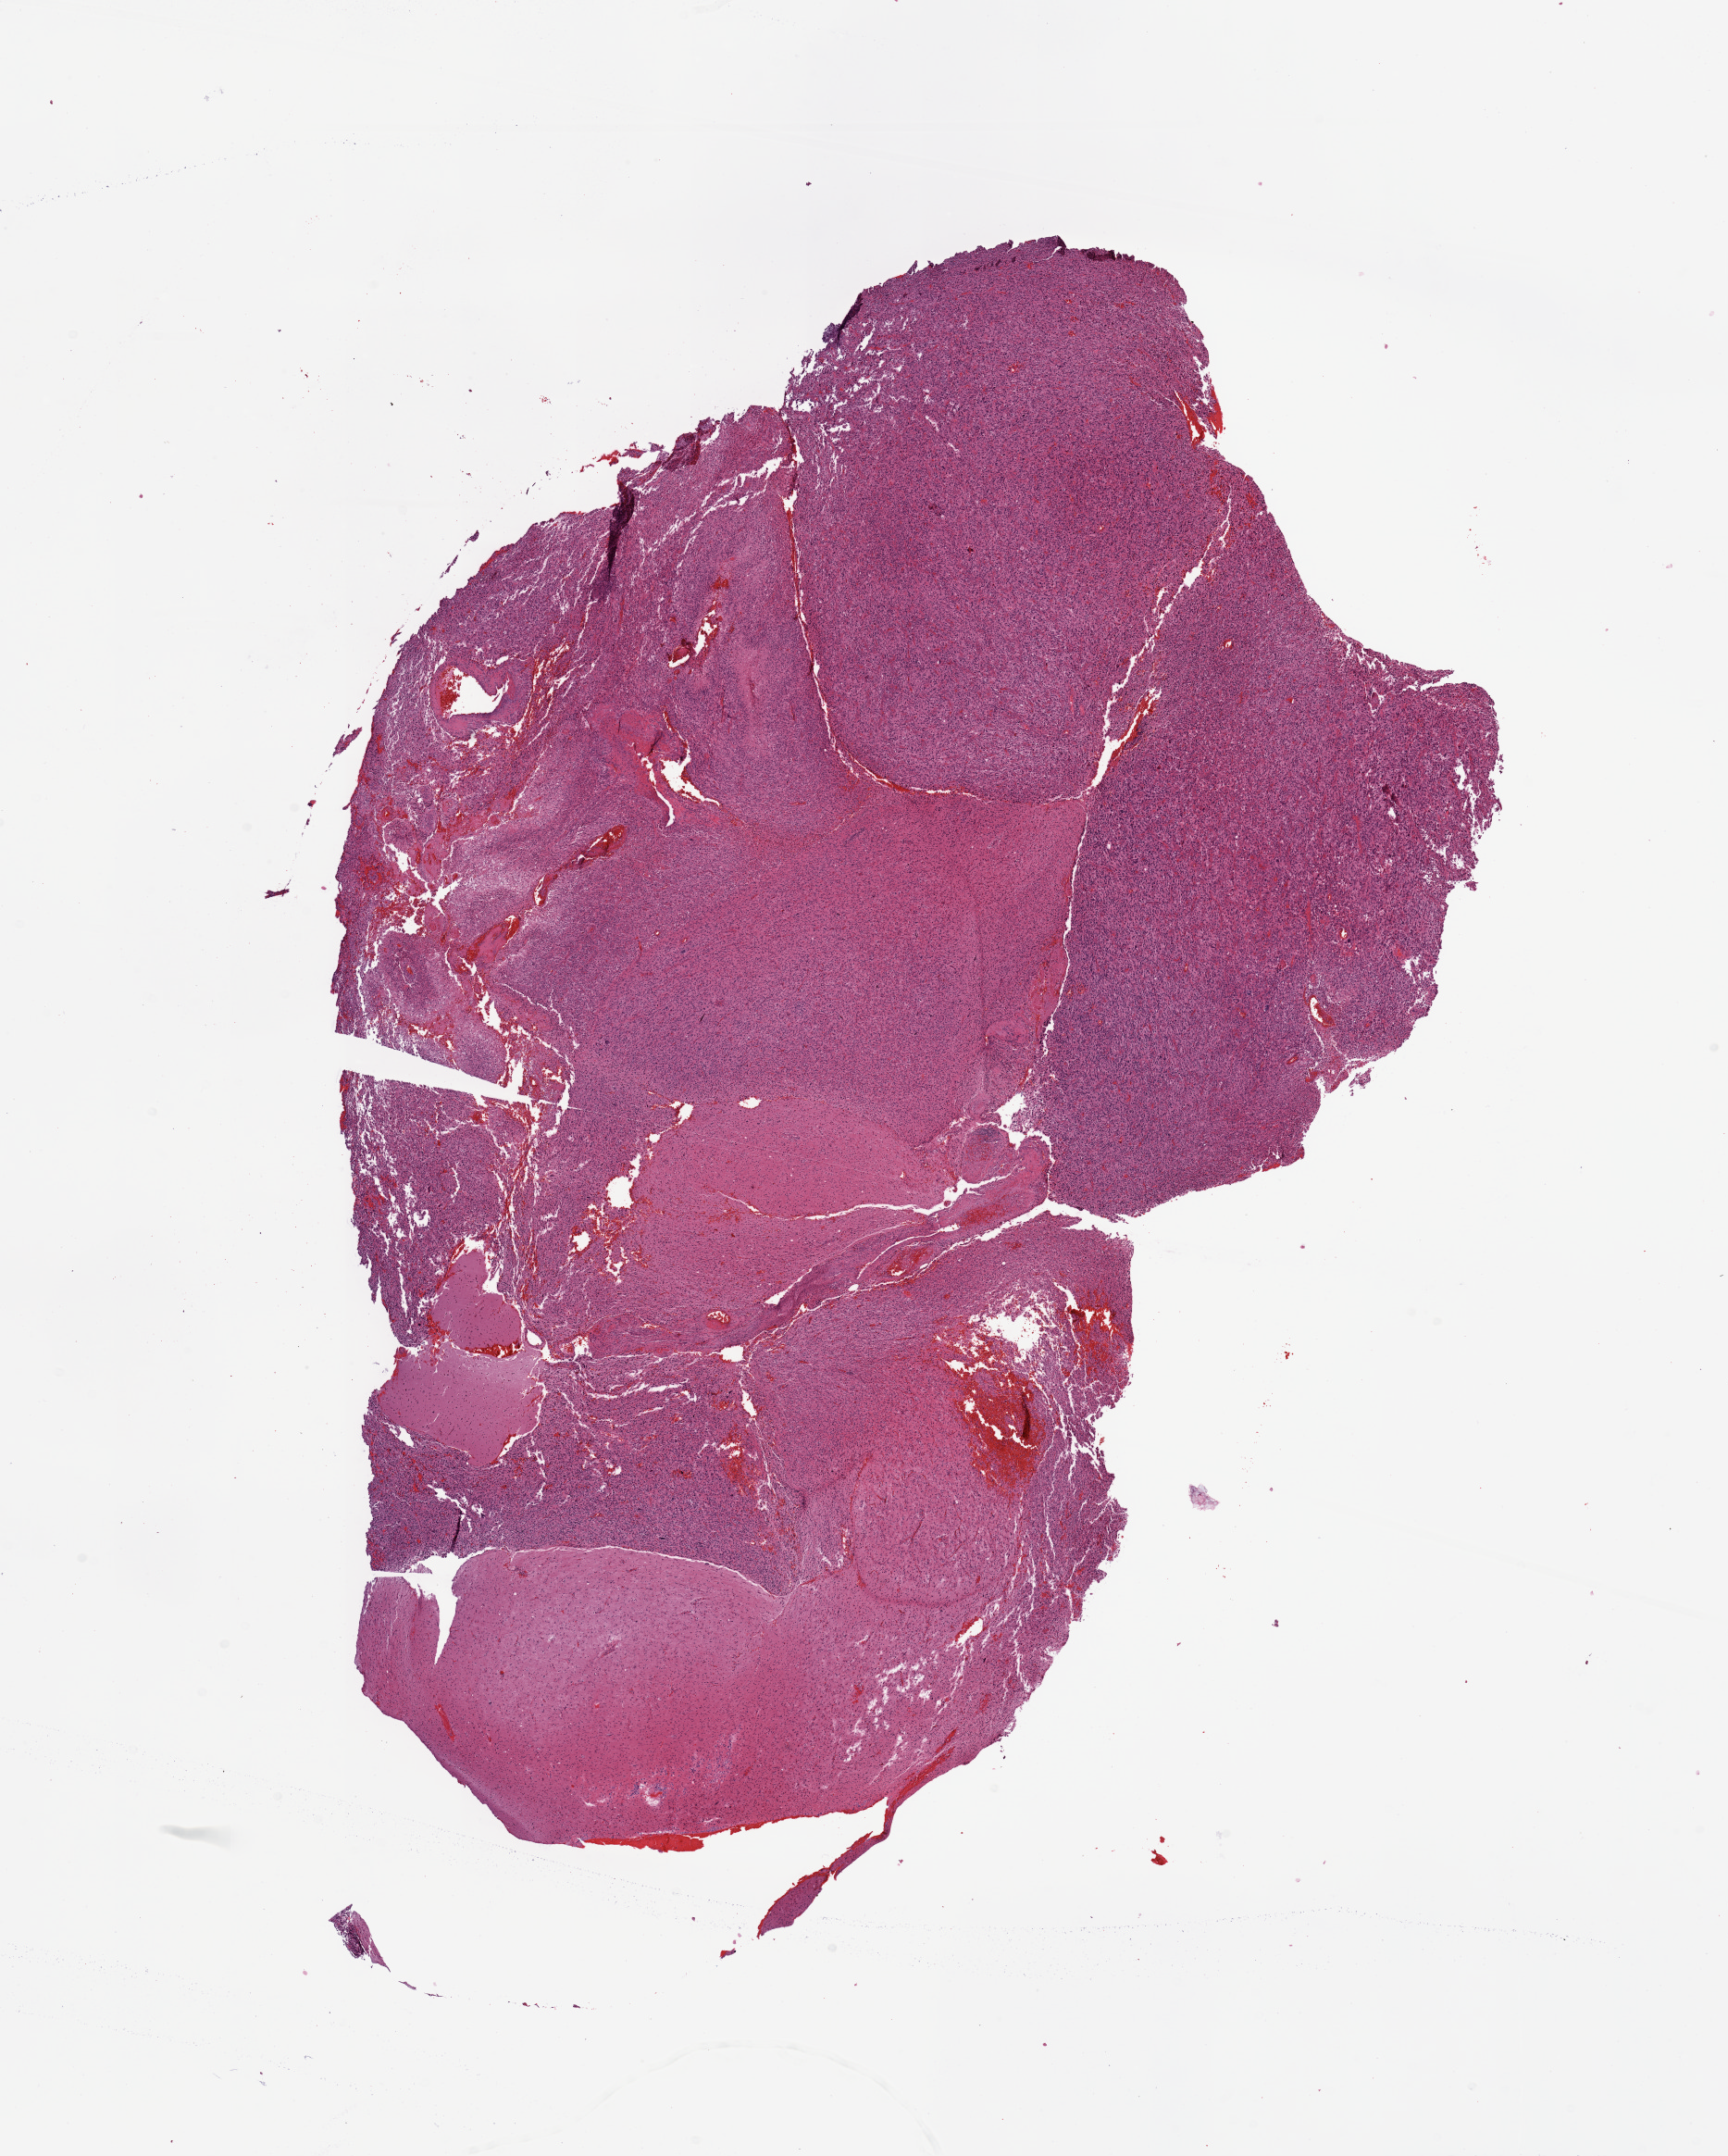
Whole-slide histology image, H&E-stained — low-resolution overview of the scanned area, about 14.8 x 18.4 mm. Brain, tumour tissue. Patient: male, age 58 years.
Diagnosis: Glioblastoma.